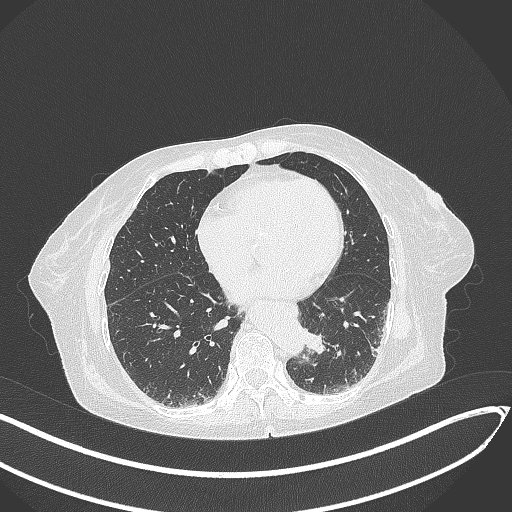
Chest CT, one axial slice. Lung window (W 1500 / L -600 HU). 1 mm slice thickness. 512 × 512 image matrix, field of view 400 × 400 mm. Patient: female, 82 years. From the clinical record (not read from this slice): clinical TNM (as recorded): T1b N0 M1.
Structures marked on this image (rectangle marked by the reading radiologist):
- lung tumour (recorded histology: adenocarcinoma): bounding box <297,323,333,357> (left, top, right, bottom; pixels)